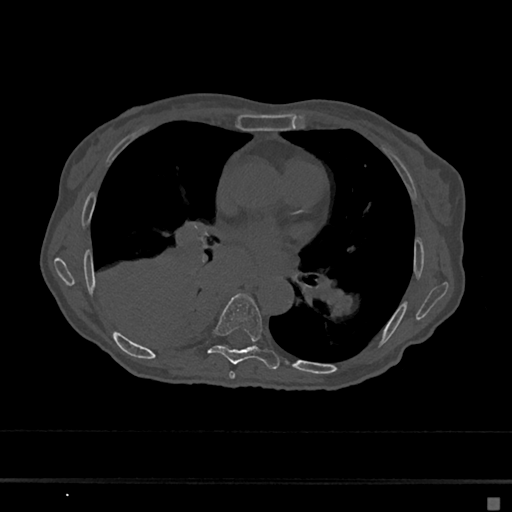
CT including the spine, one axial slice; position 371 of 797 along the scan axis; reconstruction kernel Br40s/3; 120 kVp; bone window (W 1800 / L 400 HU); 0.5 mm slice thickness; 512 × 512 image matrix, field of view 360 × 360 mm. Patient: female, 68 years. From the clinical record (not read from this slice): primary cancer: renal.
Structures marked on this image (semi-automatically segmented with operator editing):
- T6 vertebra: box from (x=229, y=371) to (x=236, y=379) px
- T7 vertebra: (x=208, y=294)–(x=280, y=370)